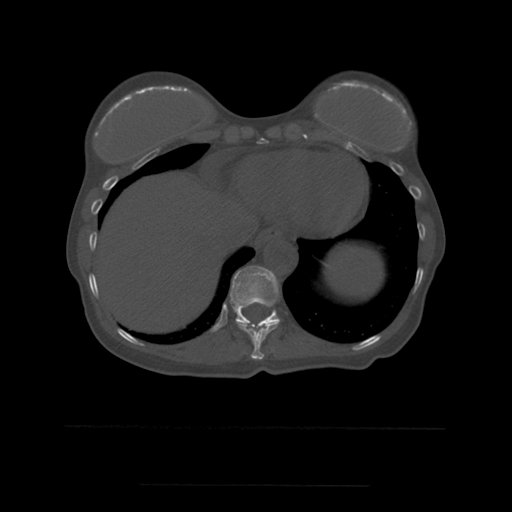
CT including the spine, one axial slice. Slice 291 of 544 in the series (ordered by position). Bone window (W 1800 / L 400 HU). 1.25 mm slice thickness. 512 × 512 image matrix, field of view 350 × 350 mm. Patient age 58 years. Case-level facts recorded for this patient, not image findings: primary cancer: lung.
Annotated regions visible in this slice (semi-automatic segmentation, software-assisted and operator-edited):
- T10 vertebra: box from (x=236, y=321) to (x=279, y=360) px
- T11 vertebra: (x=220, y=266)–(x=280, y=324)